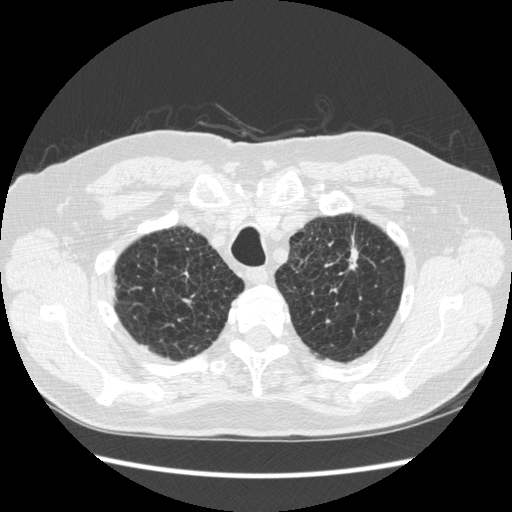
Low-dose screening chest CT, one axial slice. Position 230 of 267 along the scan axis. Reconstruction kernel STANDARD. 120 kVp. Lung window (W 1500 / L -600 HU). 512 × 512 image matrix, field of view 360 × 360 mm.
Structures marked on this image (manually delineated by an expert):
- lesion 1 (tumor, upper lobe of left lung): box from (x=349, y=245) to (x=358, y=269) px